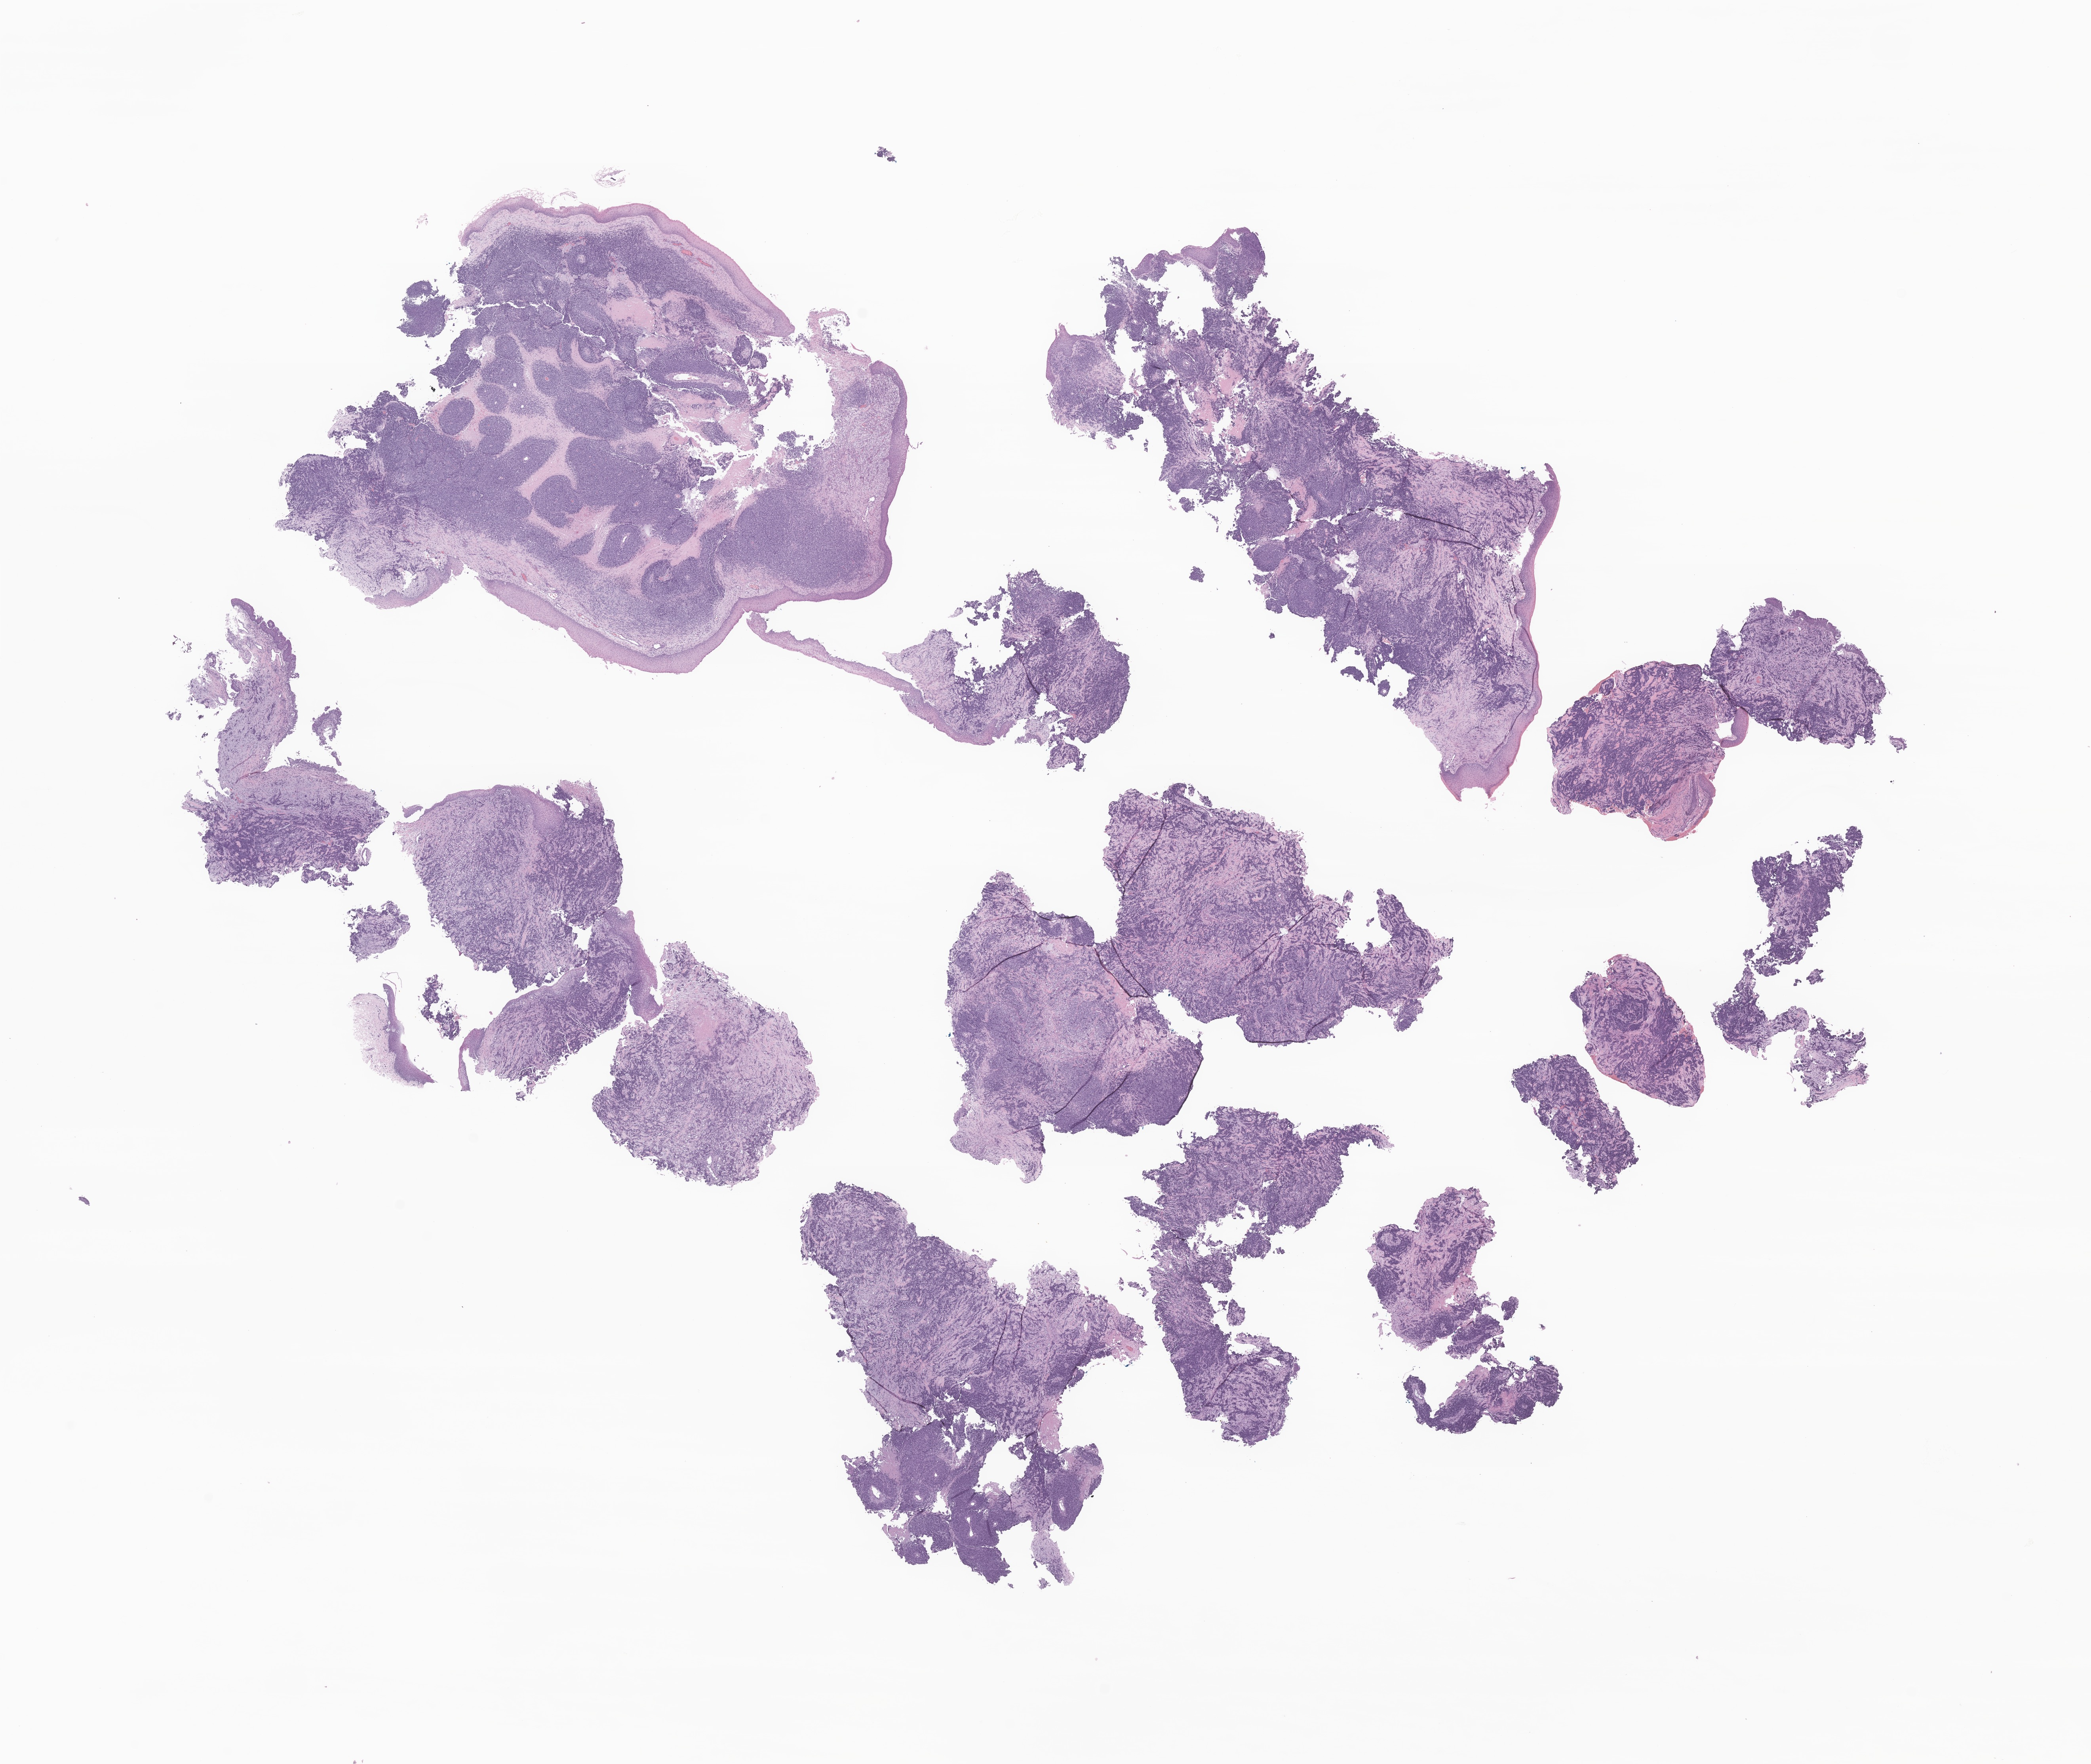
Hematoxylin and eosin (H&E) whole-slide image of tumor tissue from the nasal cavity, whole scanned area (about 22.3 x 18.8 mm) shown as a low-resolution overview; formalin-fixed, paraffin-embedded (FFPE) tissue. Patient: female, age 437 days (about 1.2 years).
* diagnosis (ICD-O-3 morphology term): Alveolar rhabdomyosarcoma